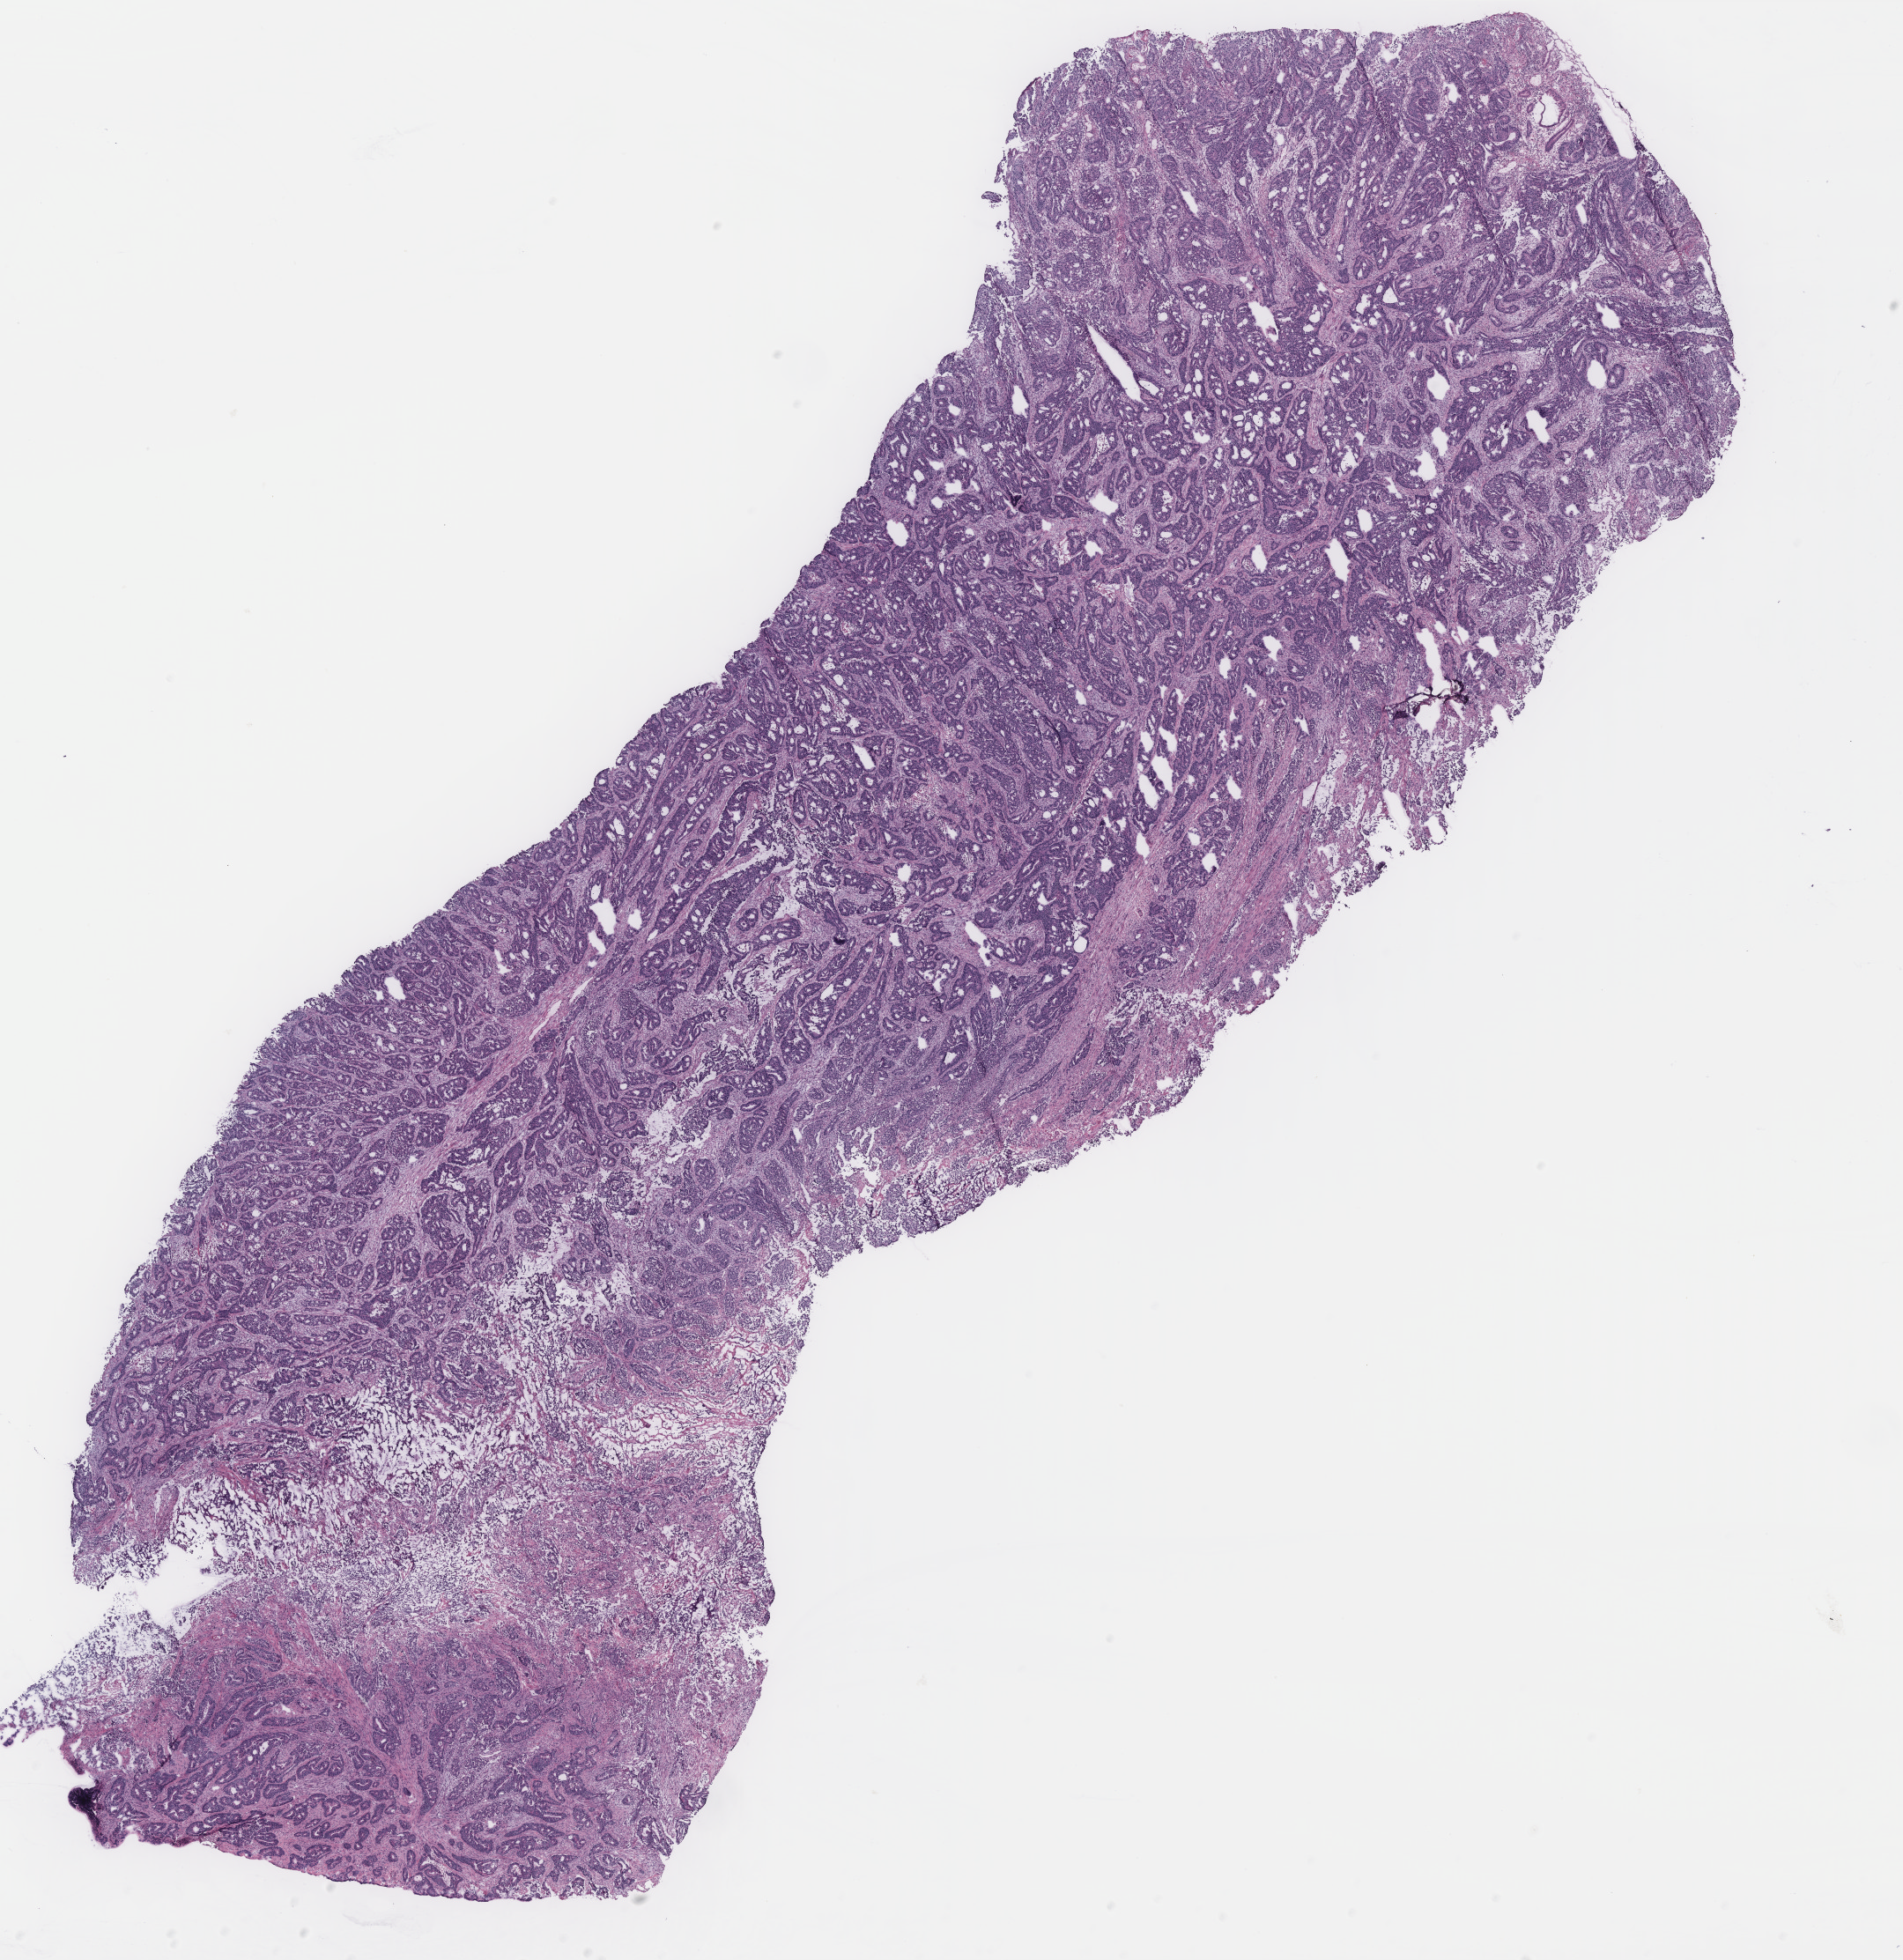
H&E whole-slide image — low-resolution overview of the scanned area, about 17.3 x 17.8 mm (from a 40x scan); colon, tissue type not recorded.
Patient diagnosis (cohort enrolment): colon cancer (colon).